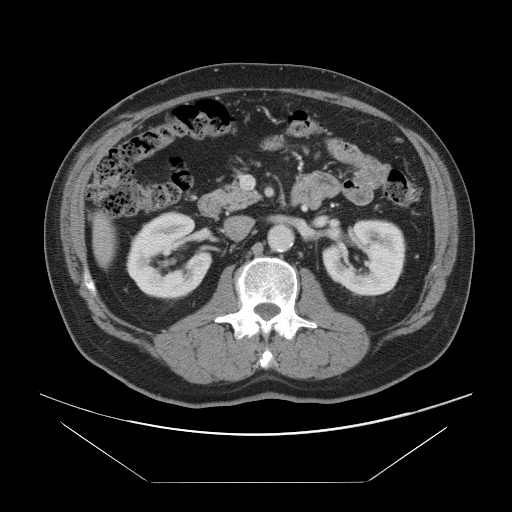
Contrast-enhanced abdominal CT, one axial slice; slice 35 of 97 in the series (ordered by position); intravenous contrast given; soft-tissue window (W 400 / L 40 HU); 5 mm slice thickness; 512 × 512 image matrix, field of view 442 × 442 mm. Male patient, age 62 years. Case-level facts recorded for this patient, not image findings: diagnosis: colorectal cancer liver metastases, imaged before liver resection; multiple liver metastases: no; largest metastasis: 7 cm; disease in both lobes: yes.
Outlined on this slice (outlined manually by an expert reader):
- liver: bounding box <95,217,115,264> (left, top, right, bottom; pixels)
- planned liver remnant (the part of the liver to remain after resection): <95,219,115,264>